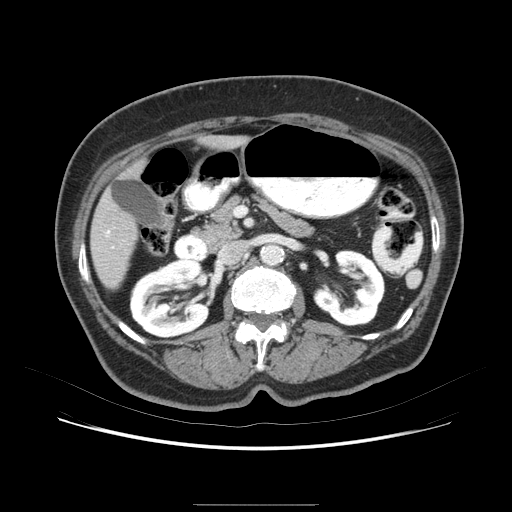
Contrast-enhanced abdominal CT (liver protocol), one axial slice; slice 28 of 79 in the series (ordered by position); 120 kVp; soft-tissue window (W 400 / L 40 HU); 2.5 mm slice thickness; 512 × 512 image matrix, field of view 380 × 380 mm. From the clinical record (not read from this slice): diagnosis: hepatocellular carcinoma (patient treated with transarterial chemoembolisation; whether this scan precedes or follows treatment is not stated here); TNM stage (as recorded): Stage-I; Child-Pugh class: A.
Outlined on this slice (semi-automatically segmented with operator editing):
- liver parenchyma outside the tumour (the mass and vessels are separate outlines, so this box may not span the whole liver): bounding box <88,130,262,305> (left, top, right, bottom; pixels)
- liver vessels: <120,209,134,272>